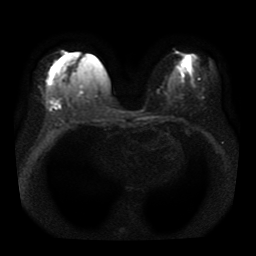
Breast MRI, one axial slice; position 18 of 41 along the scan axis; diffusion-weighted series; image 2 of 4 stored at this slice position (different b-values; order by instance number); 1.5 T; 5 mm slice thickness; 256 × 256 image matrix. Female patient.
Structures marked on this image (outlined manually by an expert reader):
- tumour on diffusion-weighted imaging: bounding box <49,99,59,106> (left, top, right, bottom; pixels)